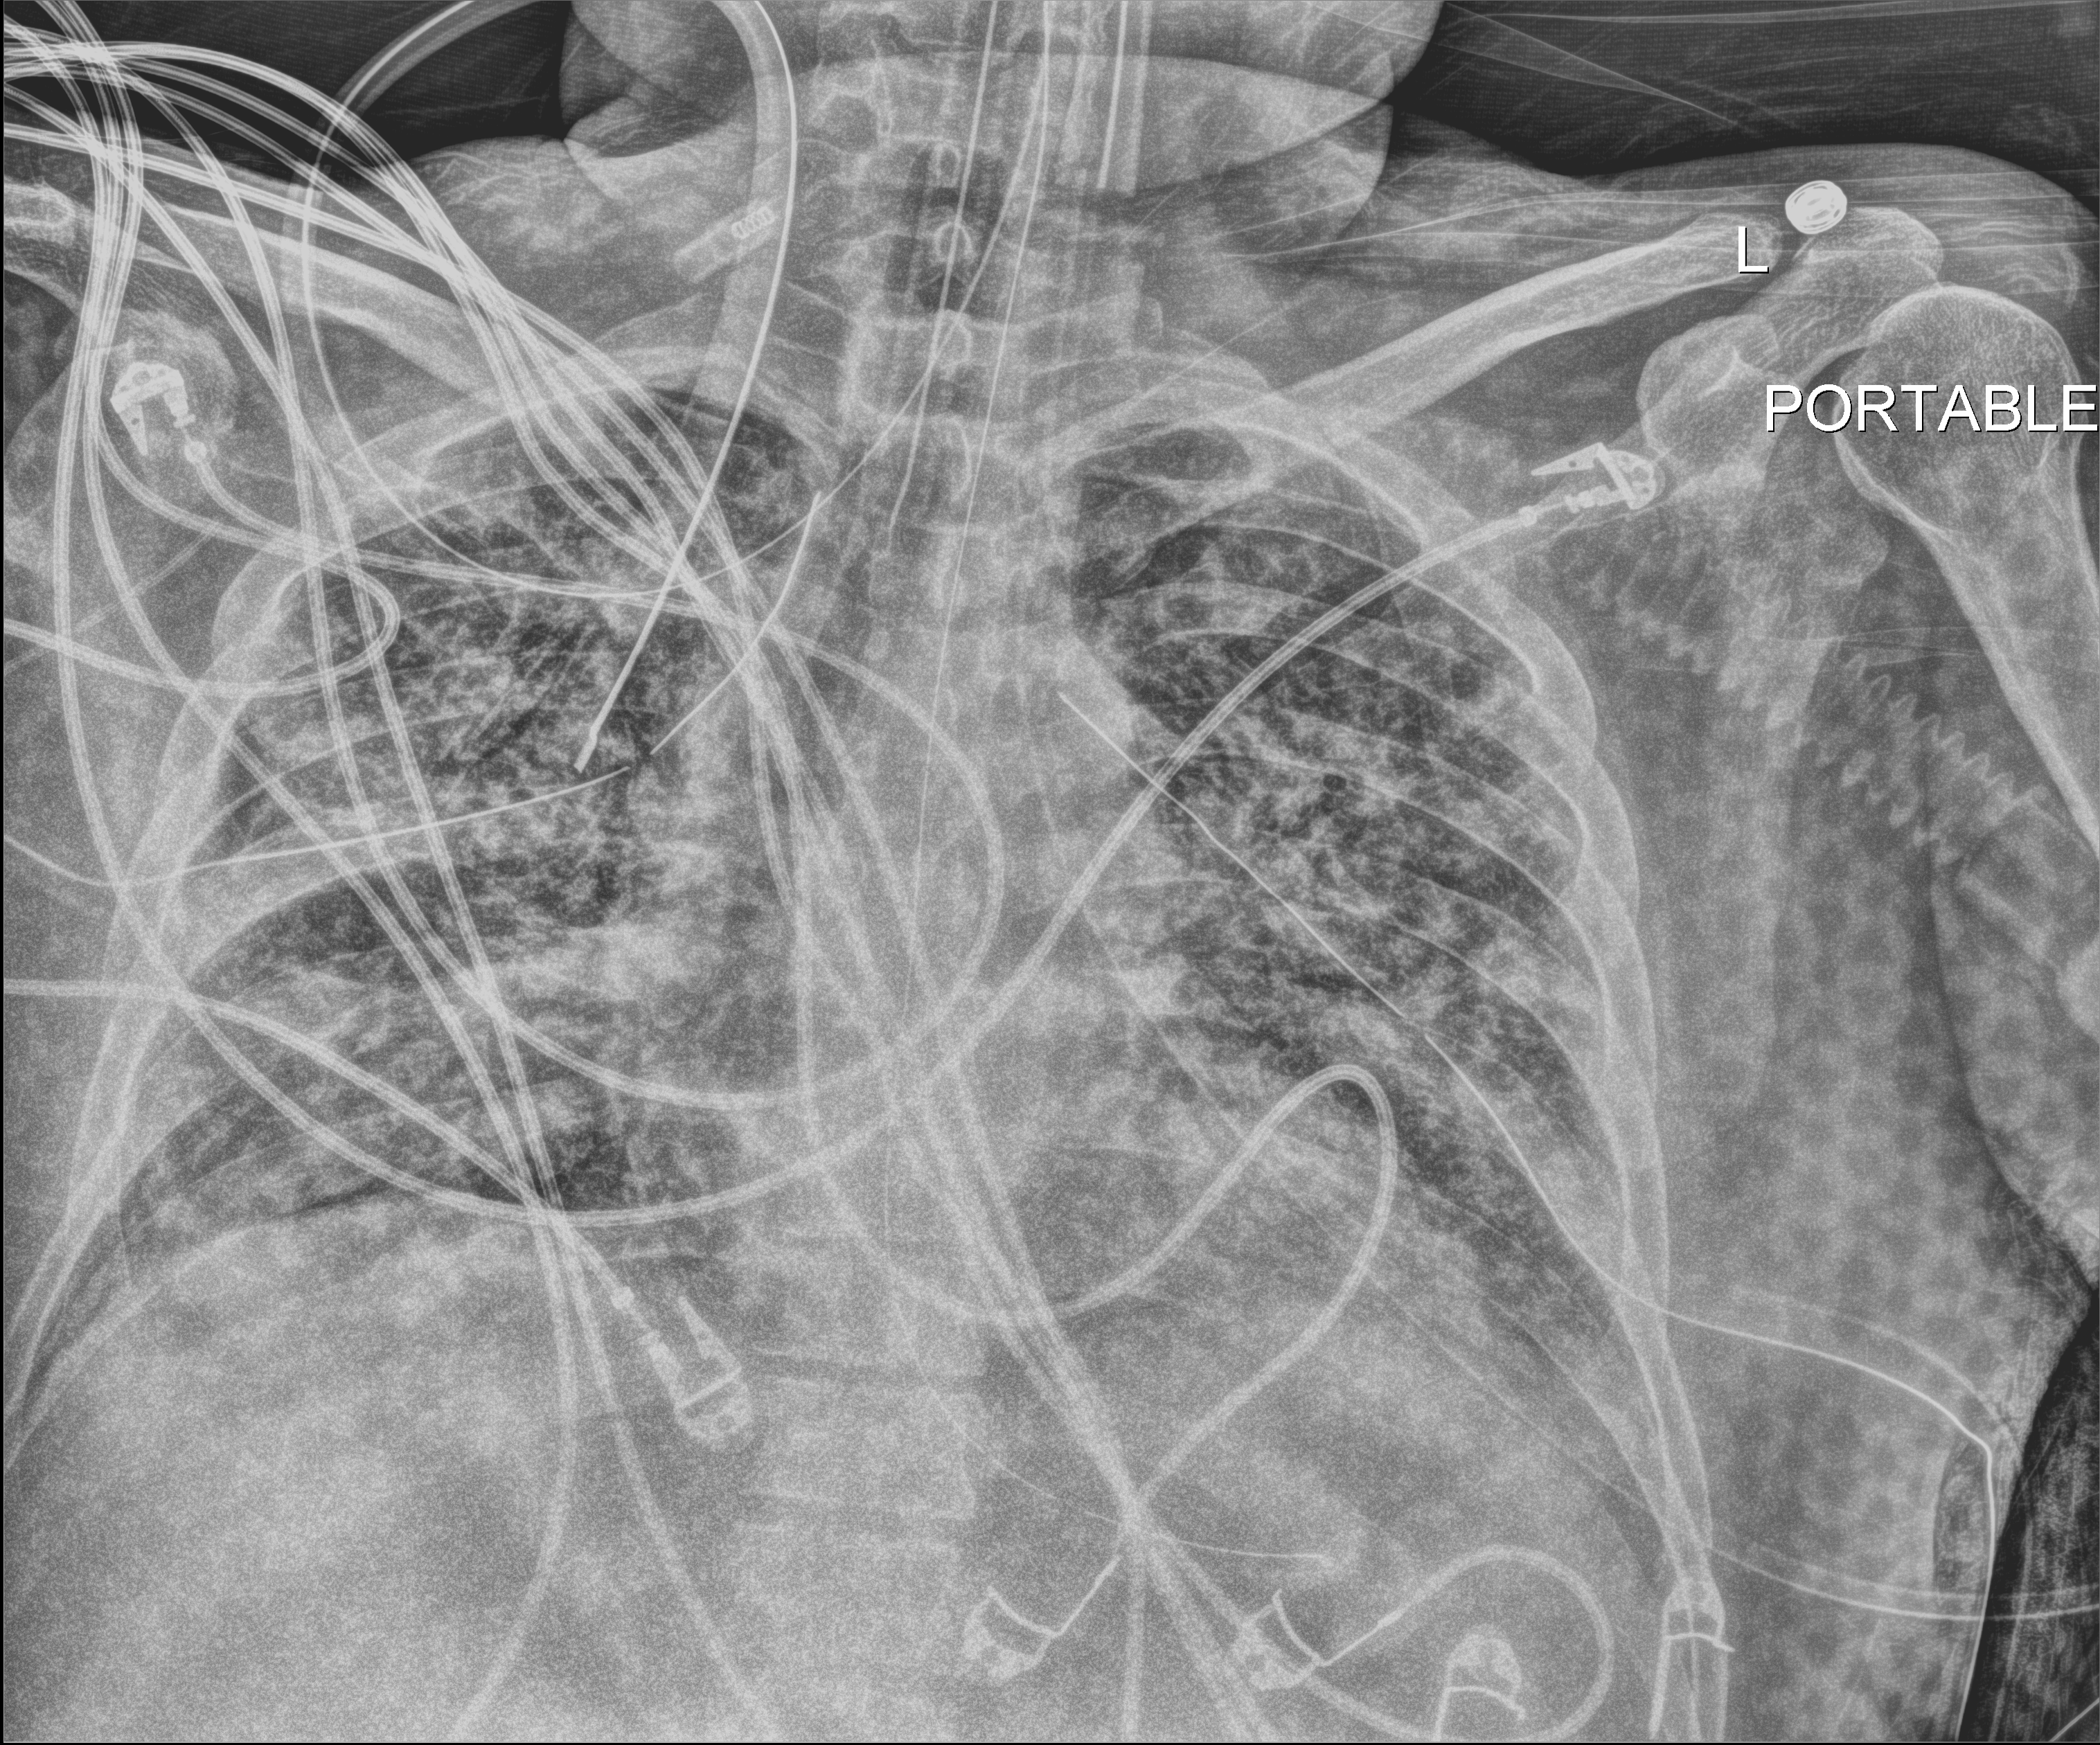
Chest X-ray (portable); anteroposterior (AP) projection. Patient hospitalised with COVID-19; male, aged 18–59 years.
Hospital-stay facts (about this admission, not read from this image; timing relative to this image not recorded): admitted to intensive care during this hospital stay: yes; hypertension (admission record): yes; mechanically ventilated during this hospital stay: yes.